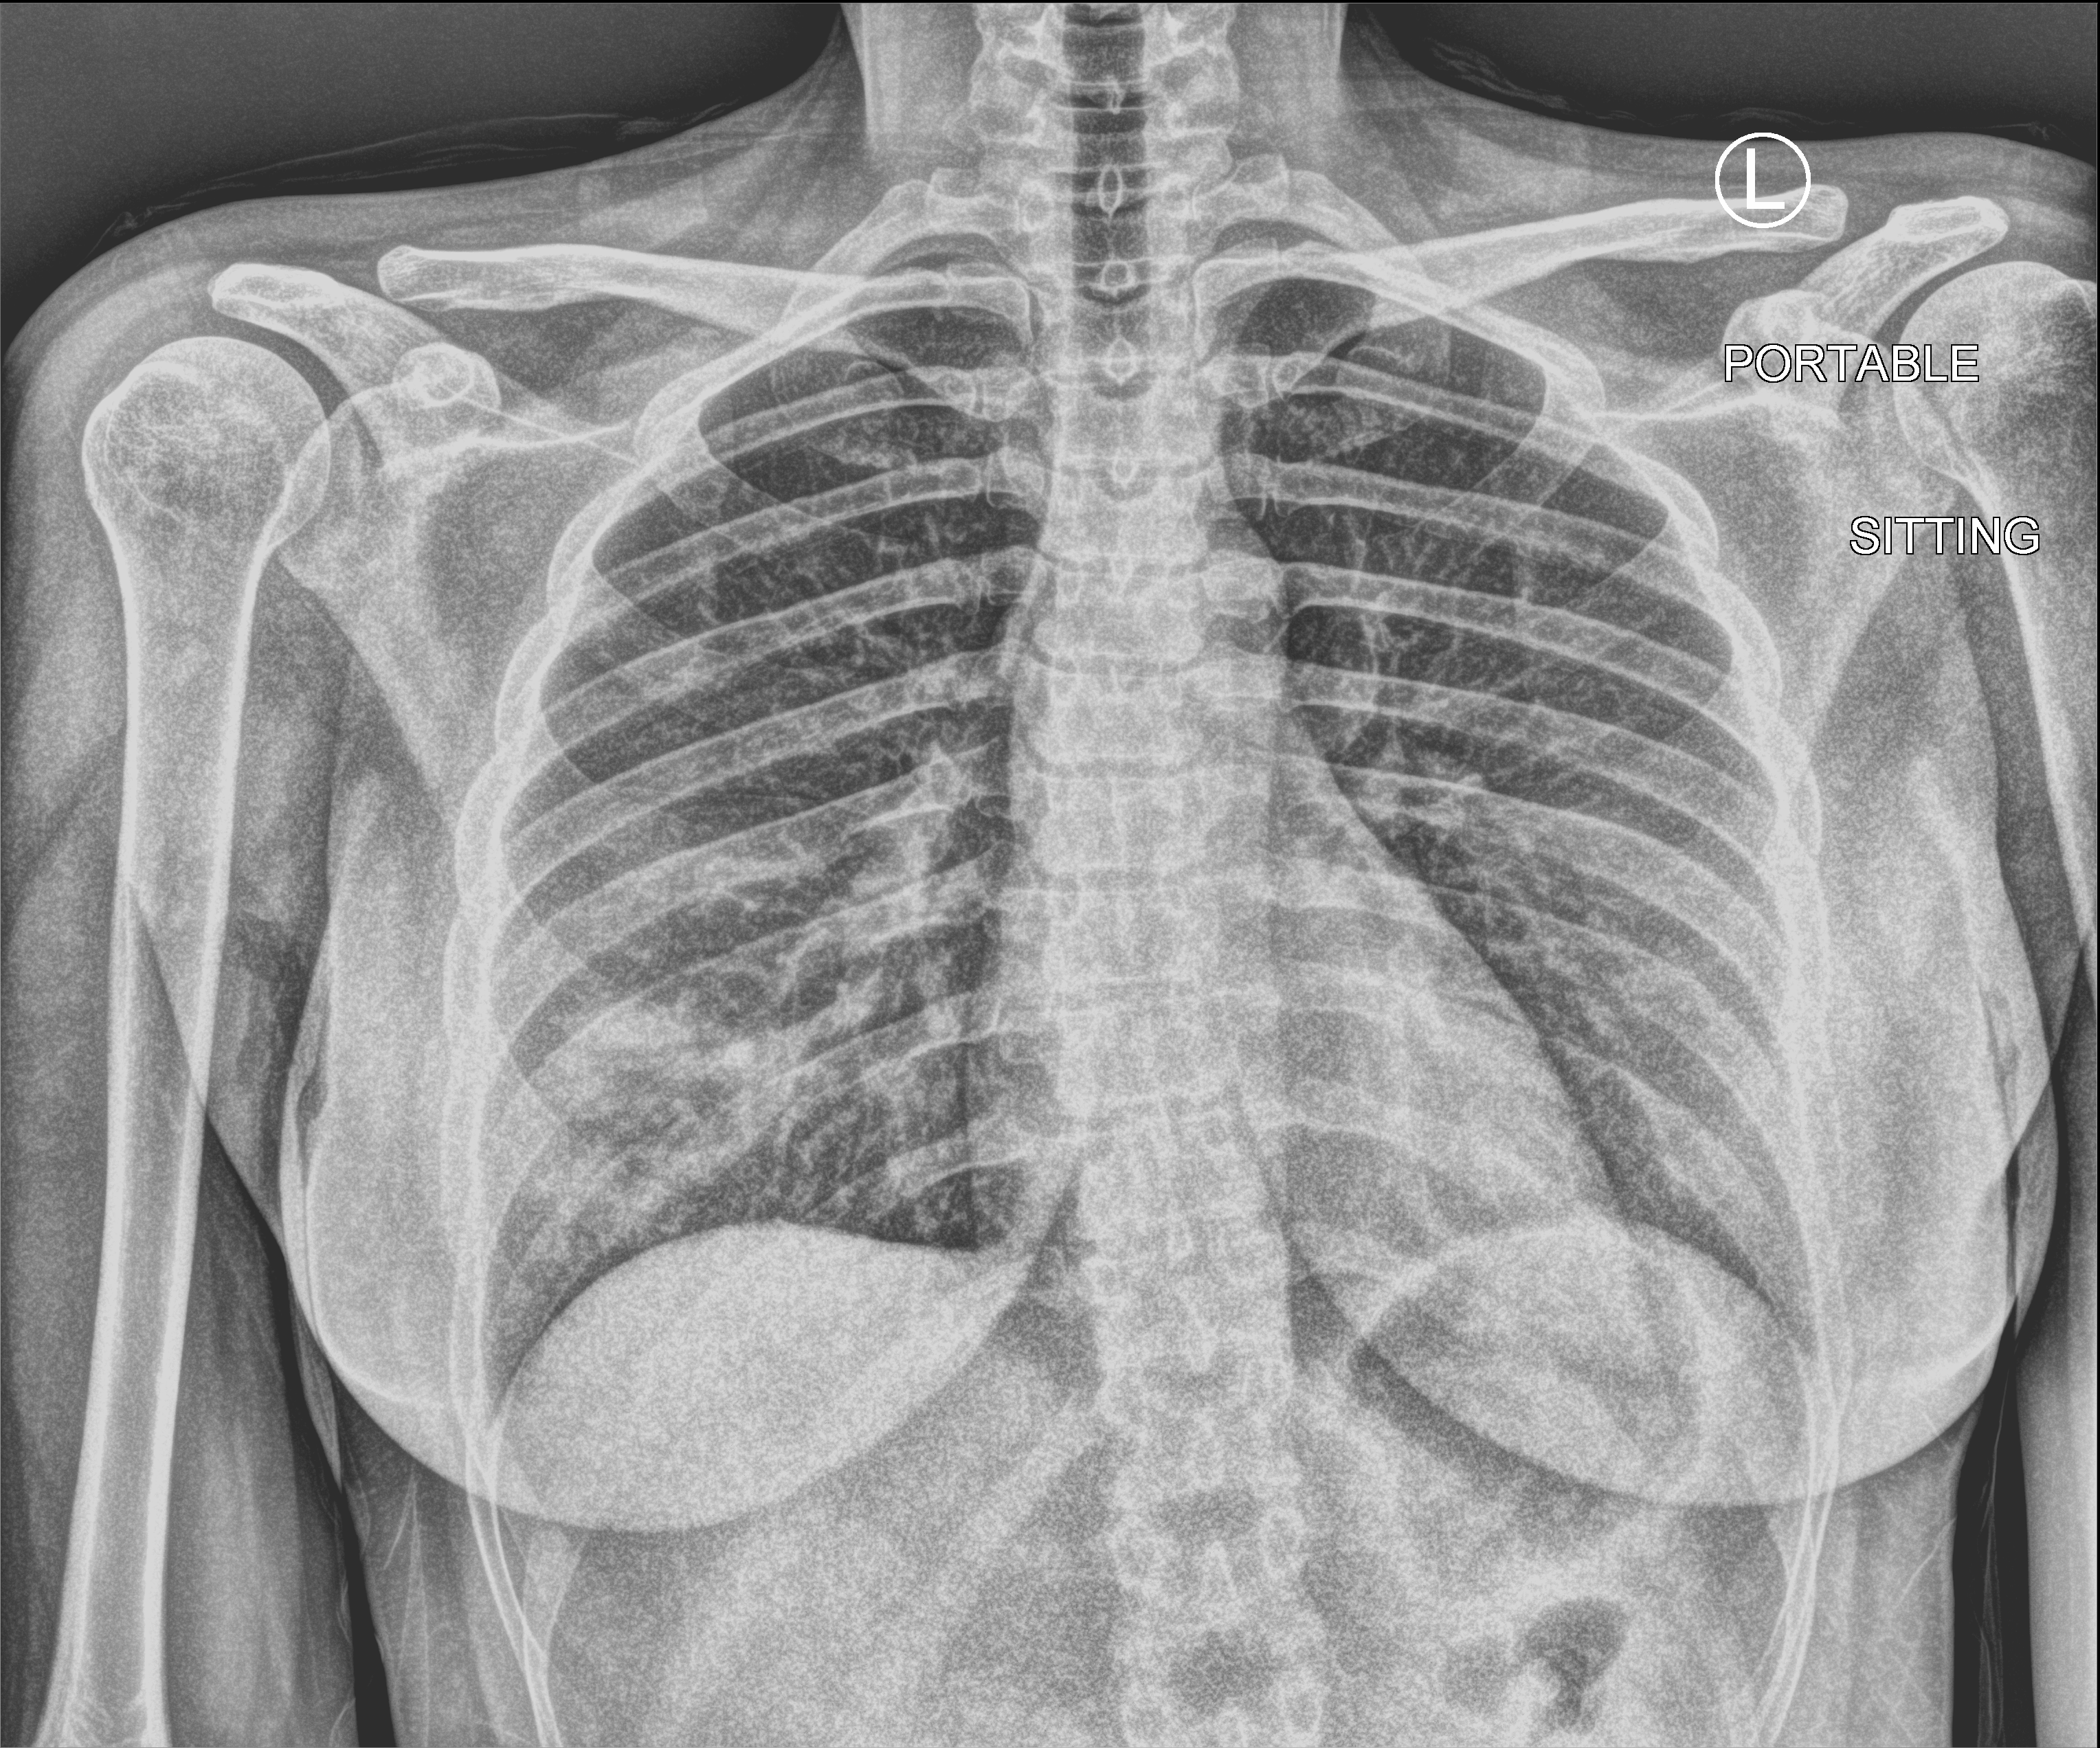
Bedside chest radiograph (computed radiography). Patient hospitalised with COVID-19; female, aged 18–59 years.
From the hospital-stay record, not from the radiograph (when in the stay this image was taken is not recorded):
- mechanically ventilated during this hospital stay: no
- length of hospital stay: 1 day
- admitted to intensive care during this hospital stay: no